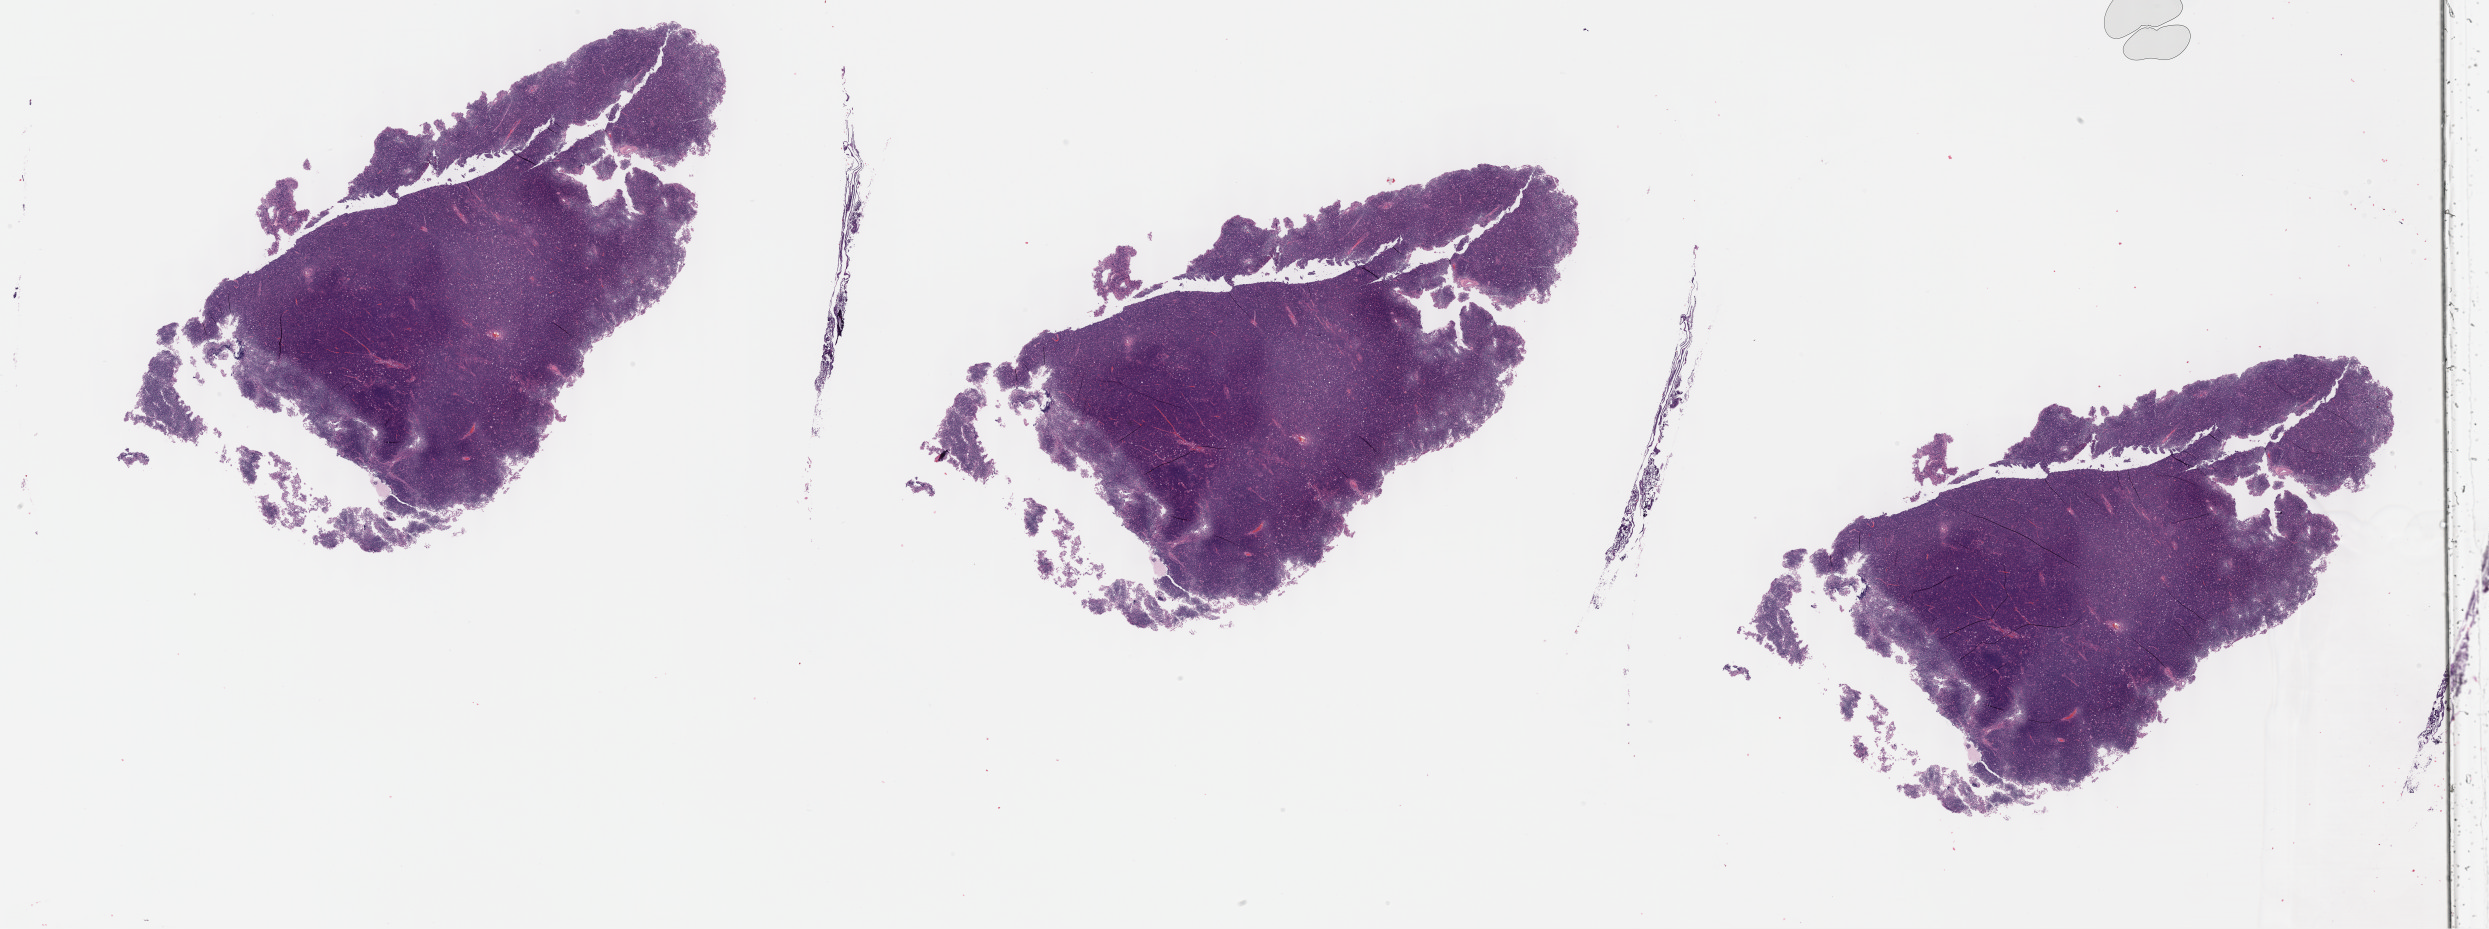
Whole-slide histology image, H&E — whole scanned area (about 40.3 x 15.0 mm) shown as a low-resolution overview, formalin-fixed paraffin-embedded (FFPE) diagnostic section, thymus, primary tumour sample. Female patient; age at initial diagnosis 71 years.
- histologic diagnosis: Thymoma, type B2, NOS (anterior mediastinum)